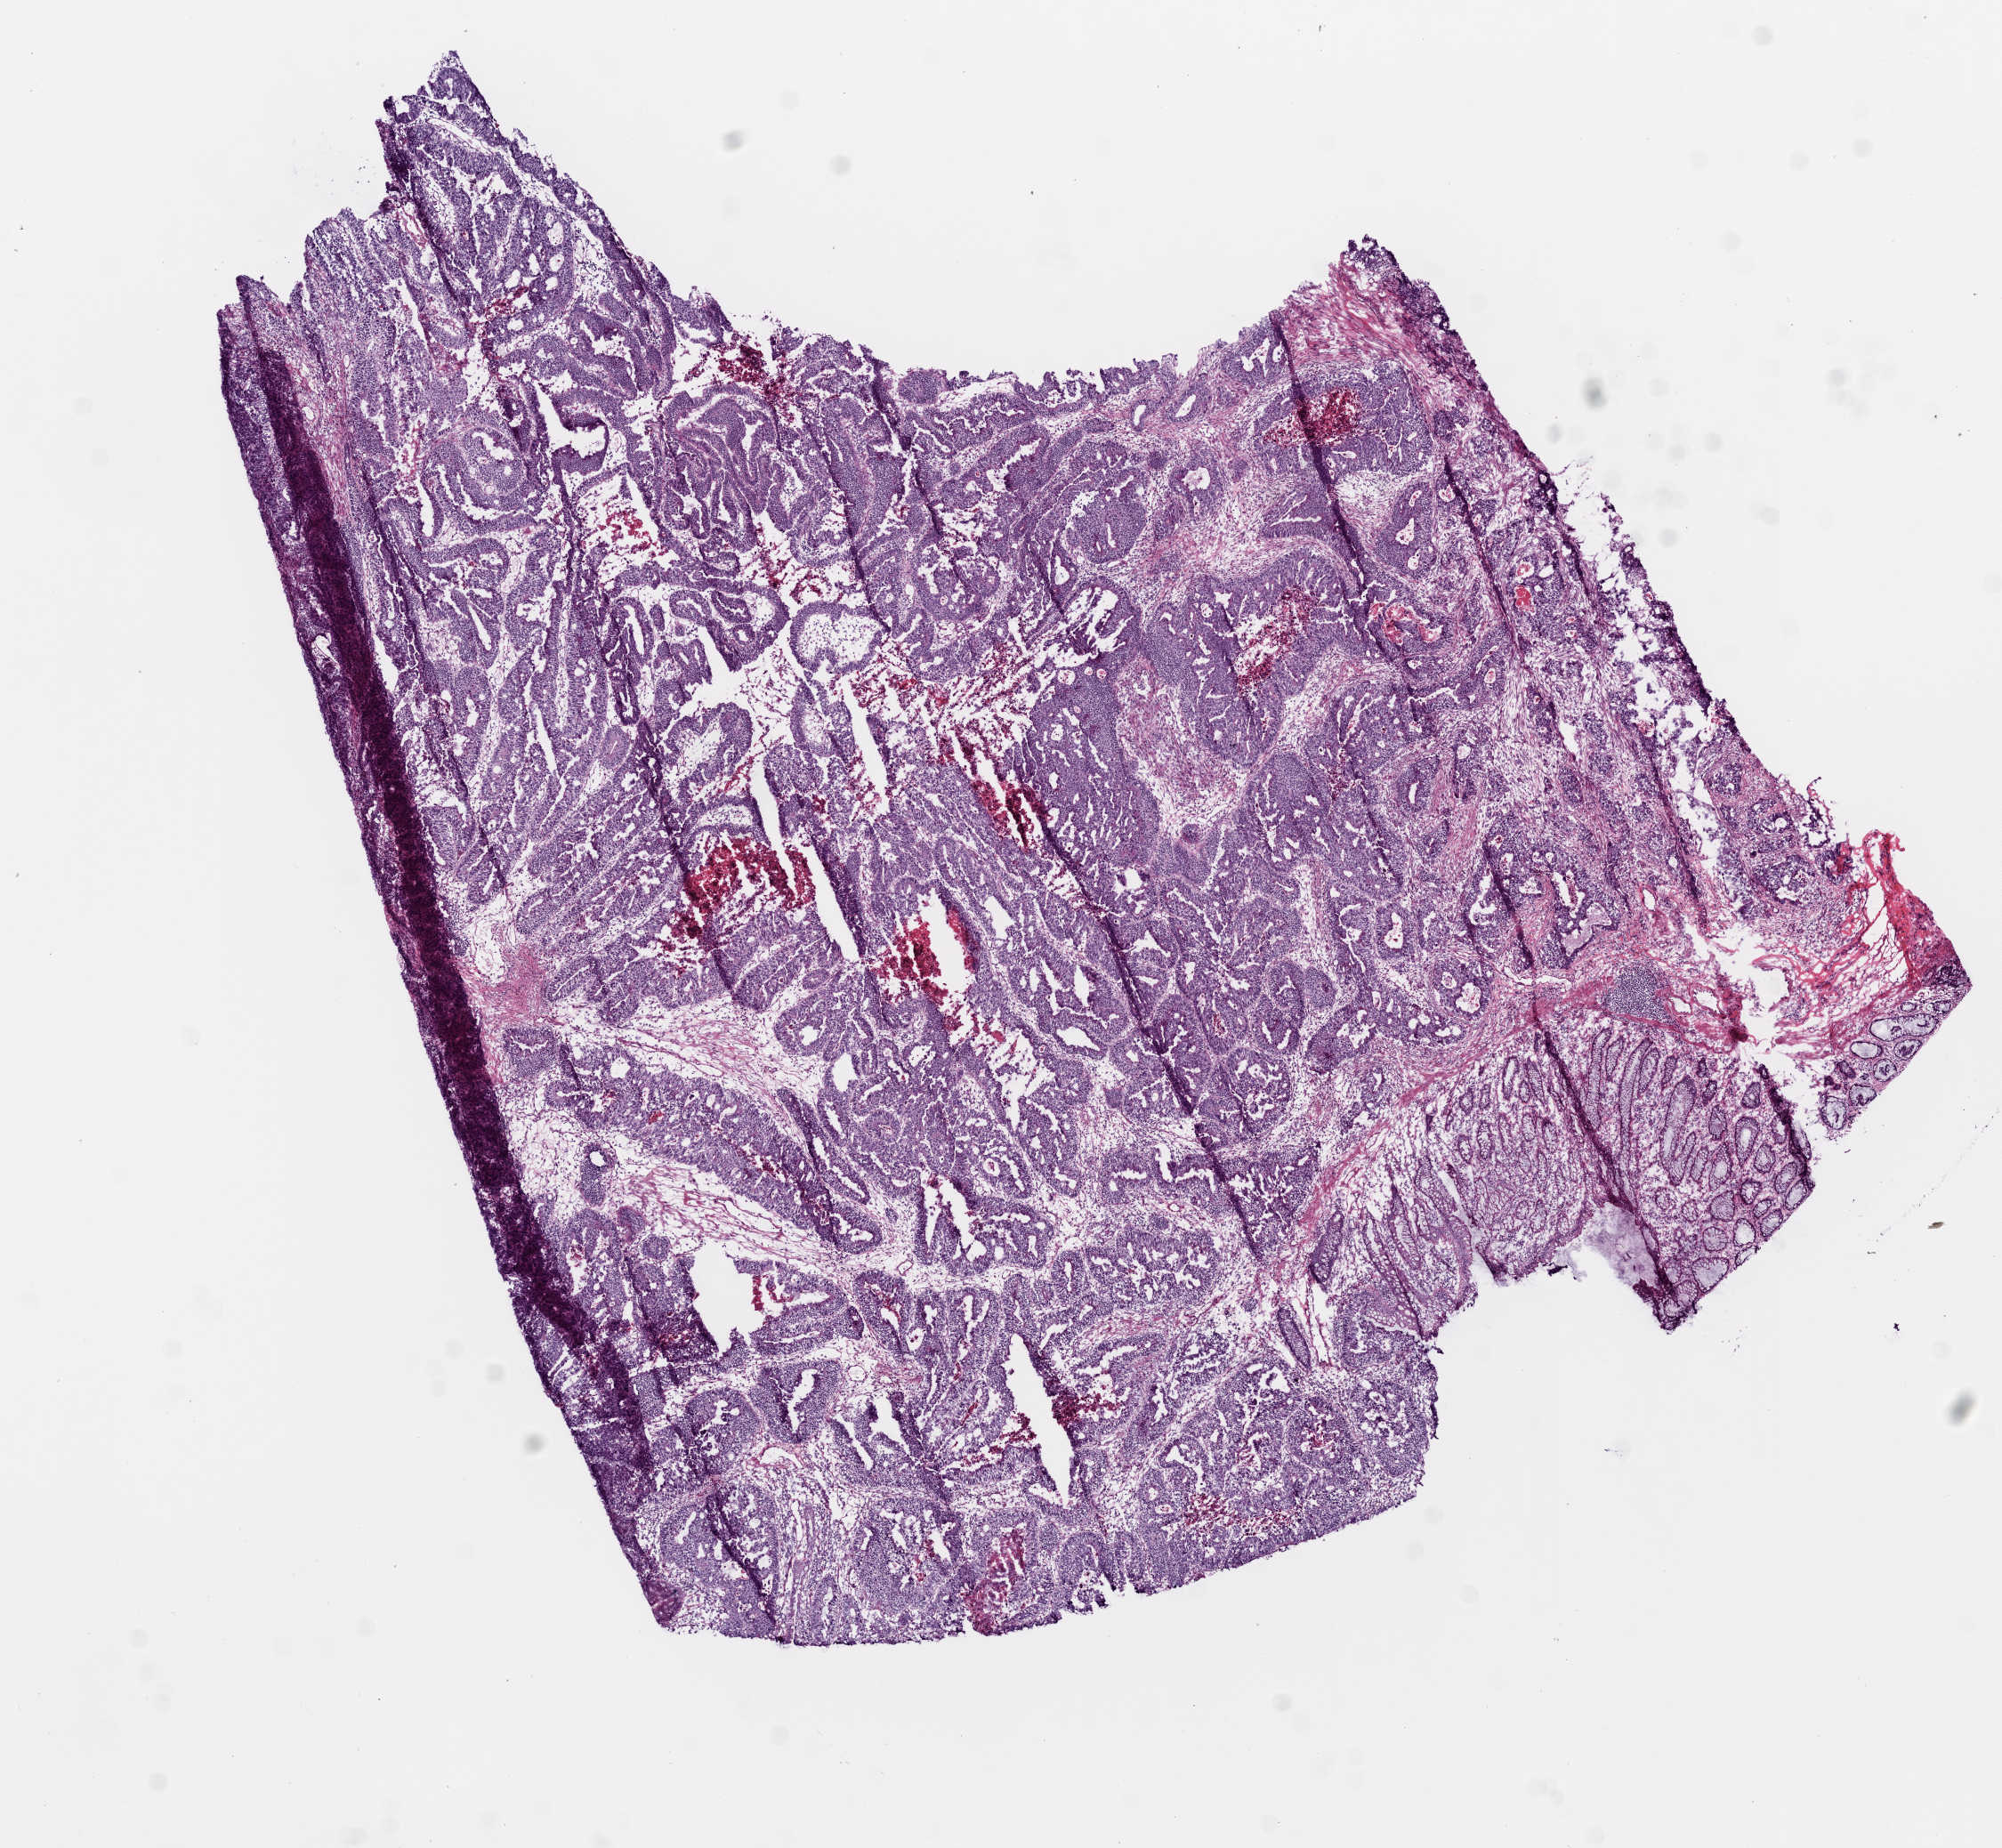
Hematoxylin and eosin (H&E) stained whole-slide image, whole scanned area (about 9.0 x 8.3 mm, acquisition: 20x scan) shown as a low-resolution overview. Frozen section from the bottom of the tissue portion. Primary tumour sample from the colon. Patient: male, age at initial diagnosis 80 years. Pathologist review of this section (percent, as recorded): tumour cells 72%, tumour nuclei 73%, normal cells 8%, stromal cells 10%, necrosis 10%.
AJCC pathologic stage: IV (6th edition). Histologic diagnosis: Adenocarcinoma, NOS.